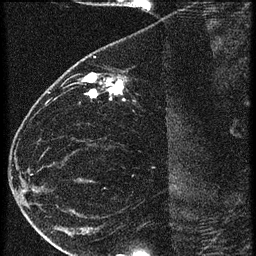
Breast MRI (dynamic contrast-enhanced), one sagittal slice. 3 images stored at this slice position (order not interpretable as contrast timing). 1.5 T. TE 4.2 ms, TR 20.4 ms. 1.5 mm slice thickness. 256 × 256 image matrix. Female patient, age 35 years. From the clinical record (not read from this slice): setting: breast cancer imaged before/during neoadjuvant chemotherapy; receptor status: HR-positive, HER2-negative.
Structures marked on this image (semi-automatically segmented with operator editing):
- analysis volume of interest (the breast-tissue region the enhancement analysis was run in; not a lesion): bounding box [x1, y1, x2, y2] px = [65, 60, 169, 119]
- tumour enhancement mask (voxels above the 90 % enhancement threshold inside the analysis volume of interest): [82, 74, 127, 99]